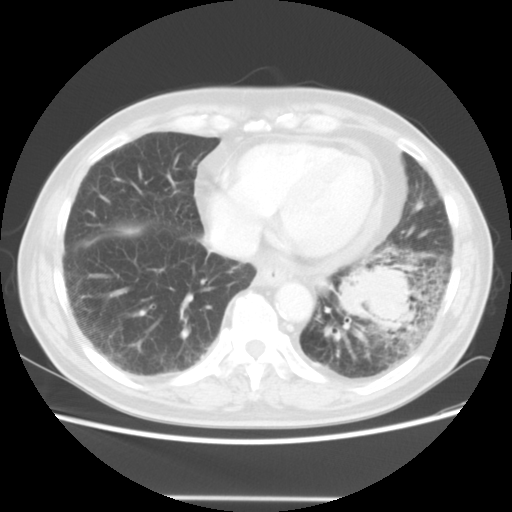
Chest CT, one axial slice; position 14 of 56 along the scan axis; reconstruction kernel STANDARD; 140 kVp; lung window (W 1500 / L -600 HU); 5 mm slice thickness; 512 × 512 image matrix. Male patient, age 66 years. Case-level facts recorded for this patient, not image findings: clinical TNM (as recorded): T4 N3 M0.
Outlined on this slice (rectangle marked by the reading radiologist):
- lung tumour (recorded histology: small cell carcinoma): bounding box [x1, y1, x2, y2] px = [328, 256, 421, 345]